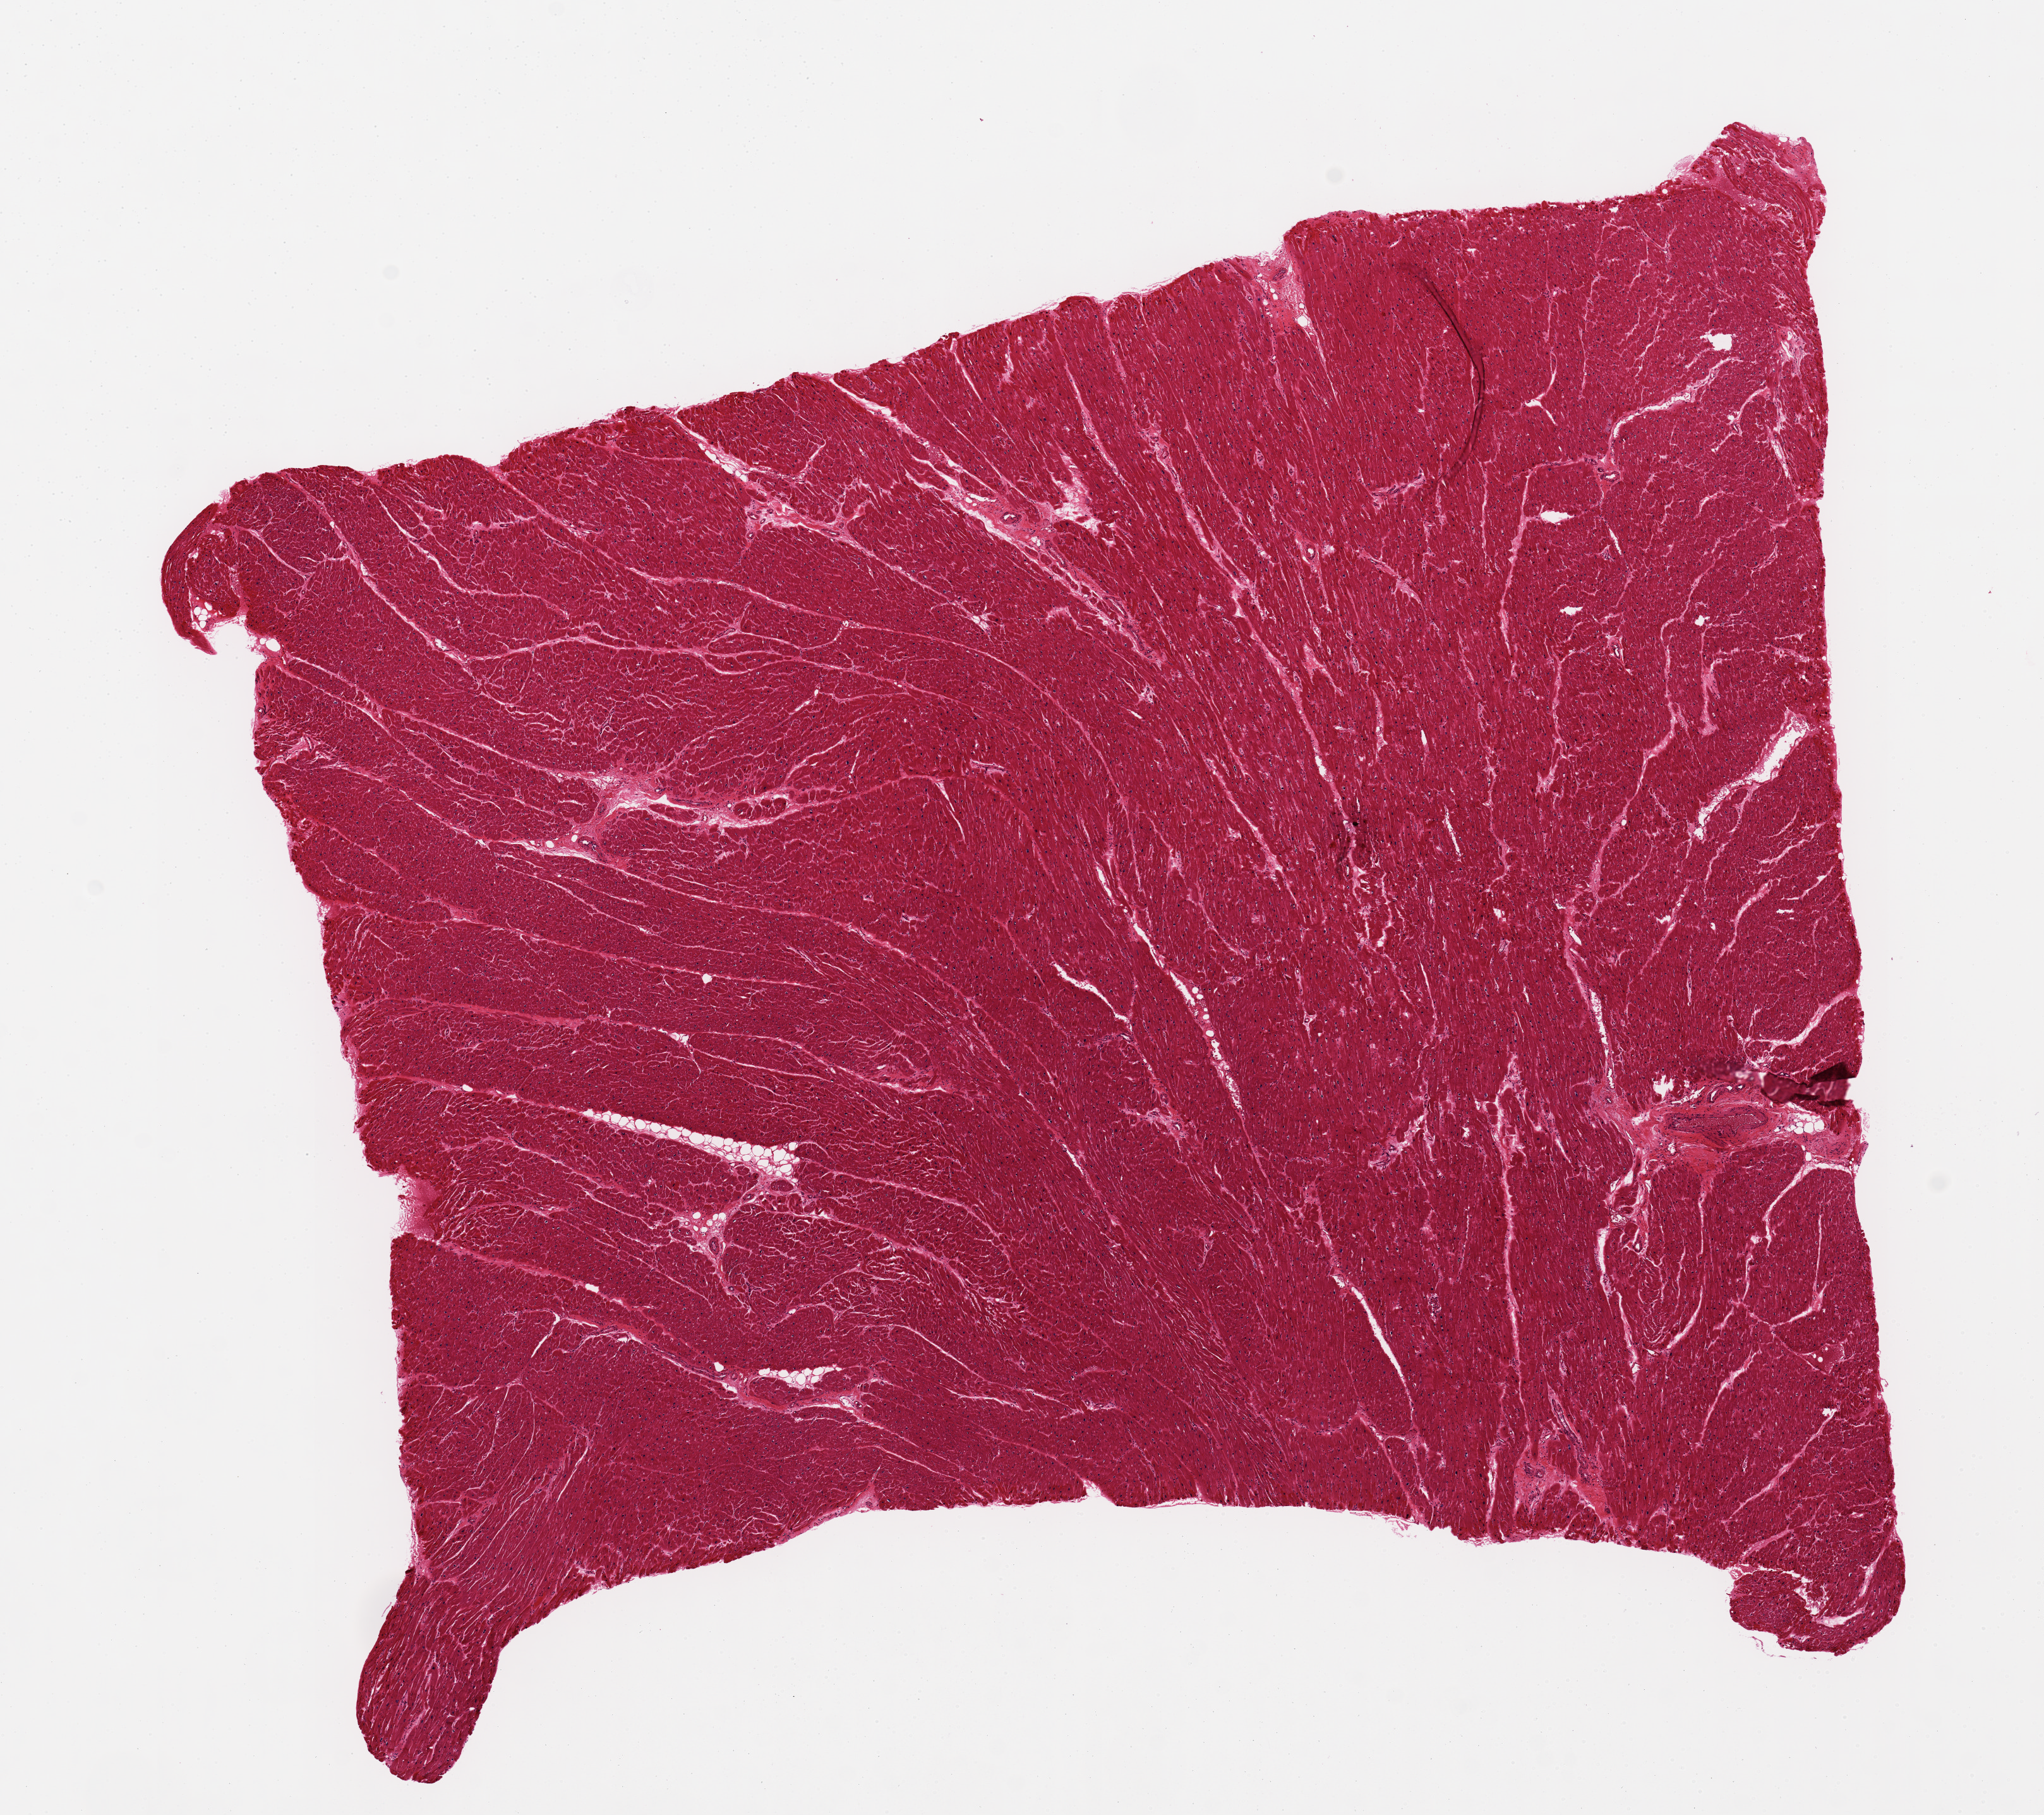
Hematoxylin and eosin (H&E) whole-slide image, low-resolution overview of the scanned area, about 12.8 x 11.4 mm (slide scanned at 20x), PAXgene-fixed, paraffin-embedded tissue, sampled site (target tissue): heart, donor tissue sample. Donor: male.
Reviewer comment on this tissue sample: 9.4x7mm. Clean specimen. Diffuse contraction bands + nuclear hypertrophy c/w mild ischemic changes.